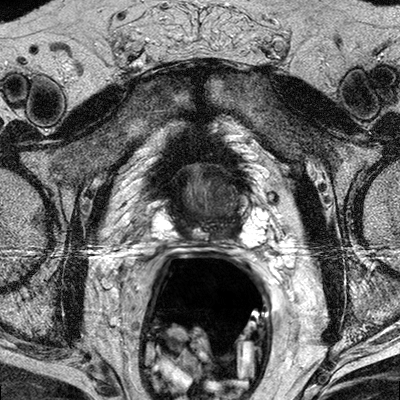
Prostate MRI examination; 3 images, each a single mid-volume slice chosen by position (not for content).
Image 1: T2-weighted axial slice, series "T2W_TSE_AX", slice 17 of 32, 3 mm slice thickness.
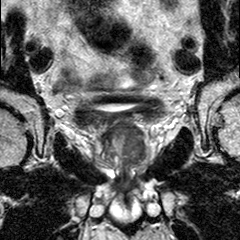
Image 2: coronal T2-weighted image, series "T2W_TSE_COR", slice 19 of 36, 3 mm slice thickness.
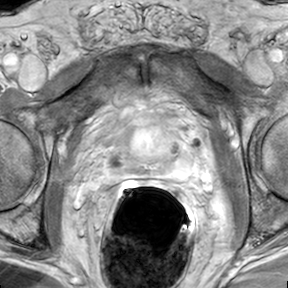
Image 3: axial dynamic contrast-enhanced (DCE) T1-weighted image, series "AX BLISS_GAD_8", slice 17 of 32, dynamic phase 5 of 8, 6 mm slice thickness.
MRI report (verbatim):
The zonal anatomy is preserved. Maximal transverse diameter 5.5 cm, maximal AP diameter 3.2 cm, and maximal craniocaudal diameter 3.5 cm. Estimated total gland volume: 32 cc. Within the left central gland nearly occupying the entire left central gland of based and mid 3rd there is a geographic homogeneously hypo intense area seen on the T2 weighted images. This area shows rapid wash in and wash out on the dynamic series and therefore is highly suspicious for prostate cancer; the mass measures 1.8 x 2.2 cm in plane, and crosses the midline; no evidence of a extra prostatic disease. No evidence of involvement of the neuro vascular bundles on either side. The seminal vesicles are collapsed and therefore the assessment is not optimal. However no evidence of manifest seminal vesicle infiltration. No enlarged obturator or iliac lymph nodes on either side. IMPRESSION: 2.2 cm left central gland mass, crossing the midline ; no evidence of extra prostatic disease. No pelvic lymphadenopathy.

Prostate biopsy pathology (as recorded):
PROSTATE: 1. RIGHT PZ: PROSTATIC TISSUE, NO TUMOR IDENTIFIED. 2. RIGHT PZ/TZ: PROSTATIC TISSUE WITH CHRONIC INFLAMMATION. NO TUMOR IDENTIFIED. 3. RIGHT APEX: PROSTATIC TISSUE WITH CHRONIC INFLAMMATION. NO TUMOR IDENTIFIED. 4. LEFT PZ: PROSTATIC TISSUE WITH CHRONIC INFLAMMATION. NO TUMOR IDENTIFIED. 5. LEFT PZ/TZ: PROSTATIC ADENOCARCINOMA, GLEASON SCORE 3+3=6/10, INVOLVING 10% OF TISSUE SUBMITTED. 6. LEFT APEX: STROMAL TISSUE ONLY. NO TUMOR IDENTIFIED.